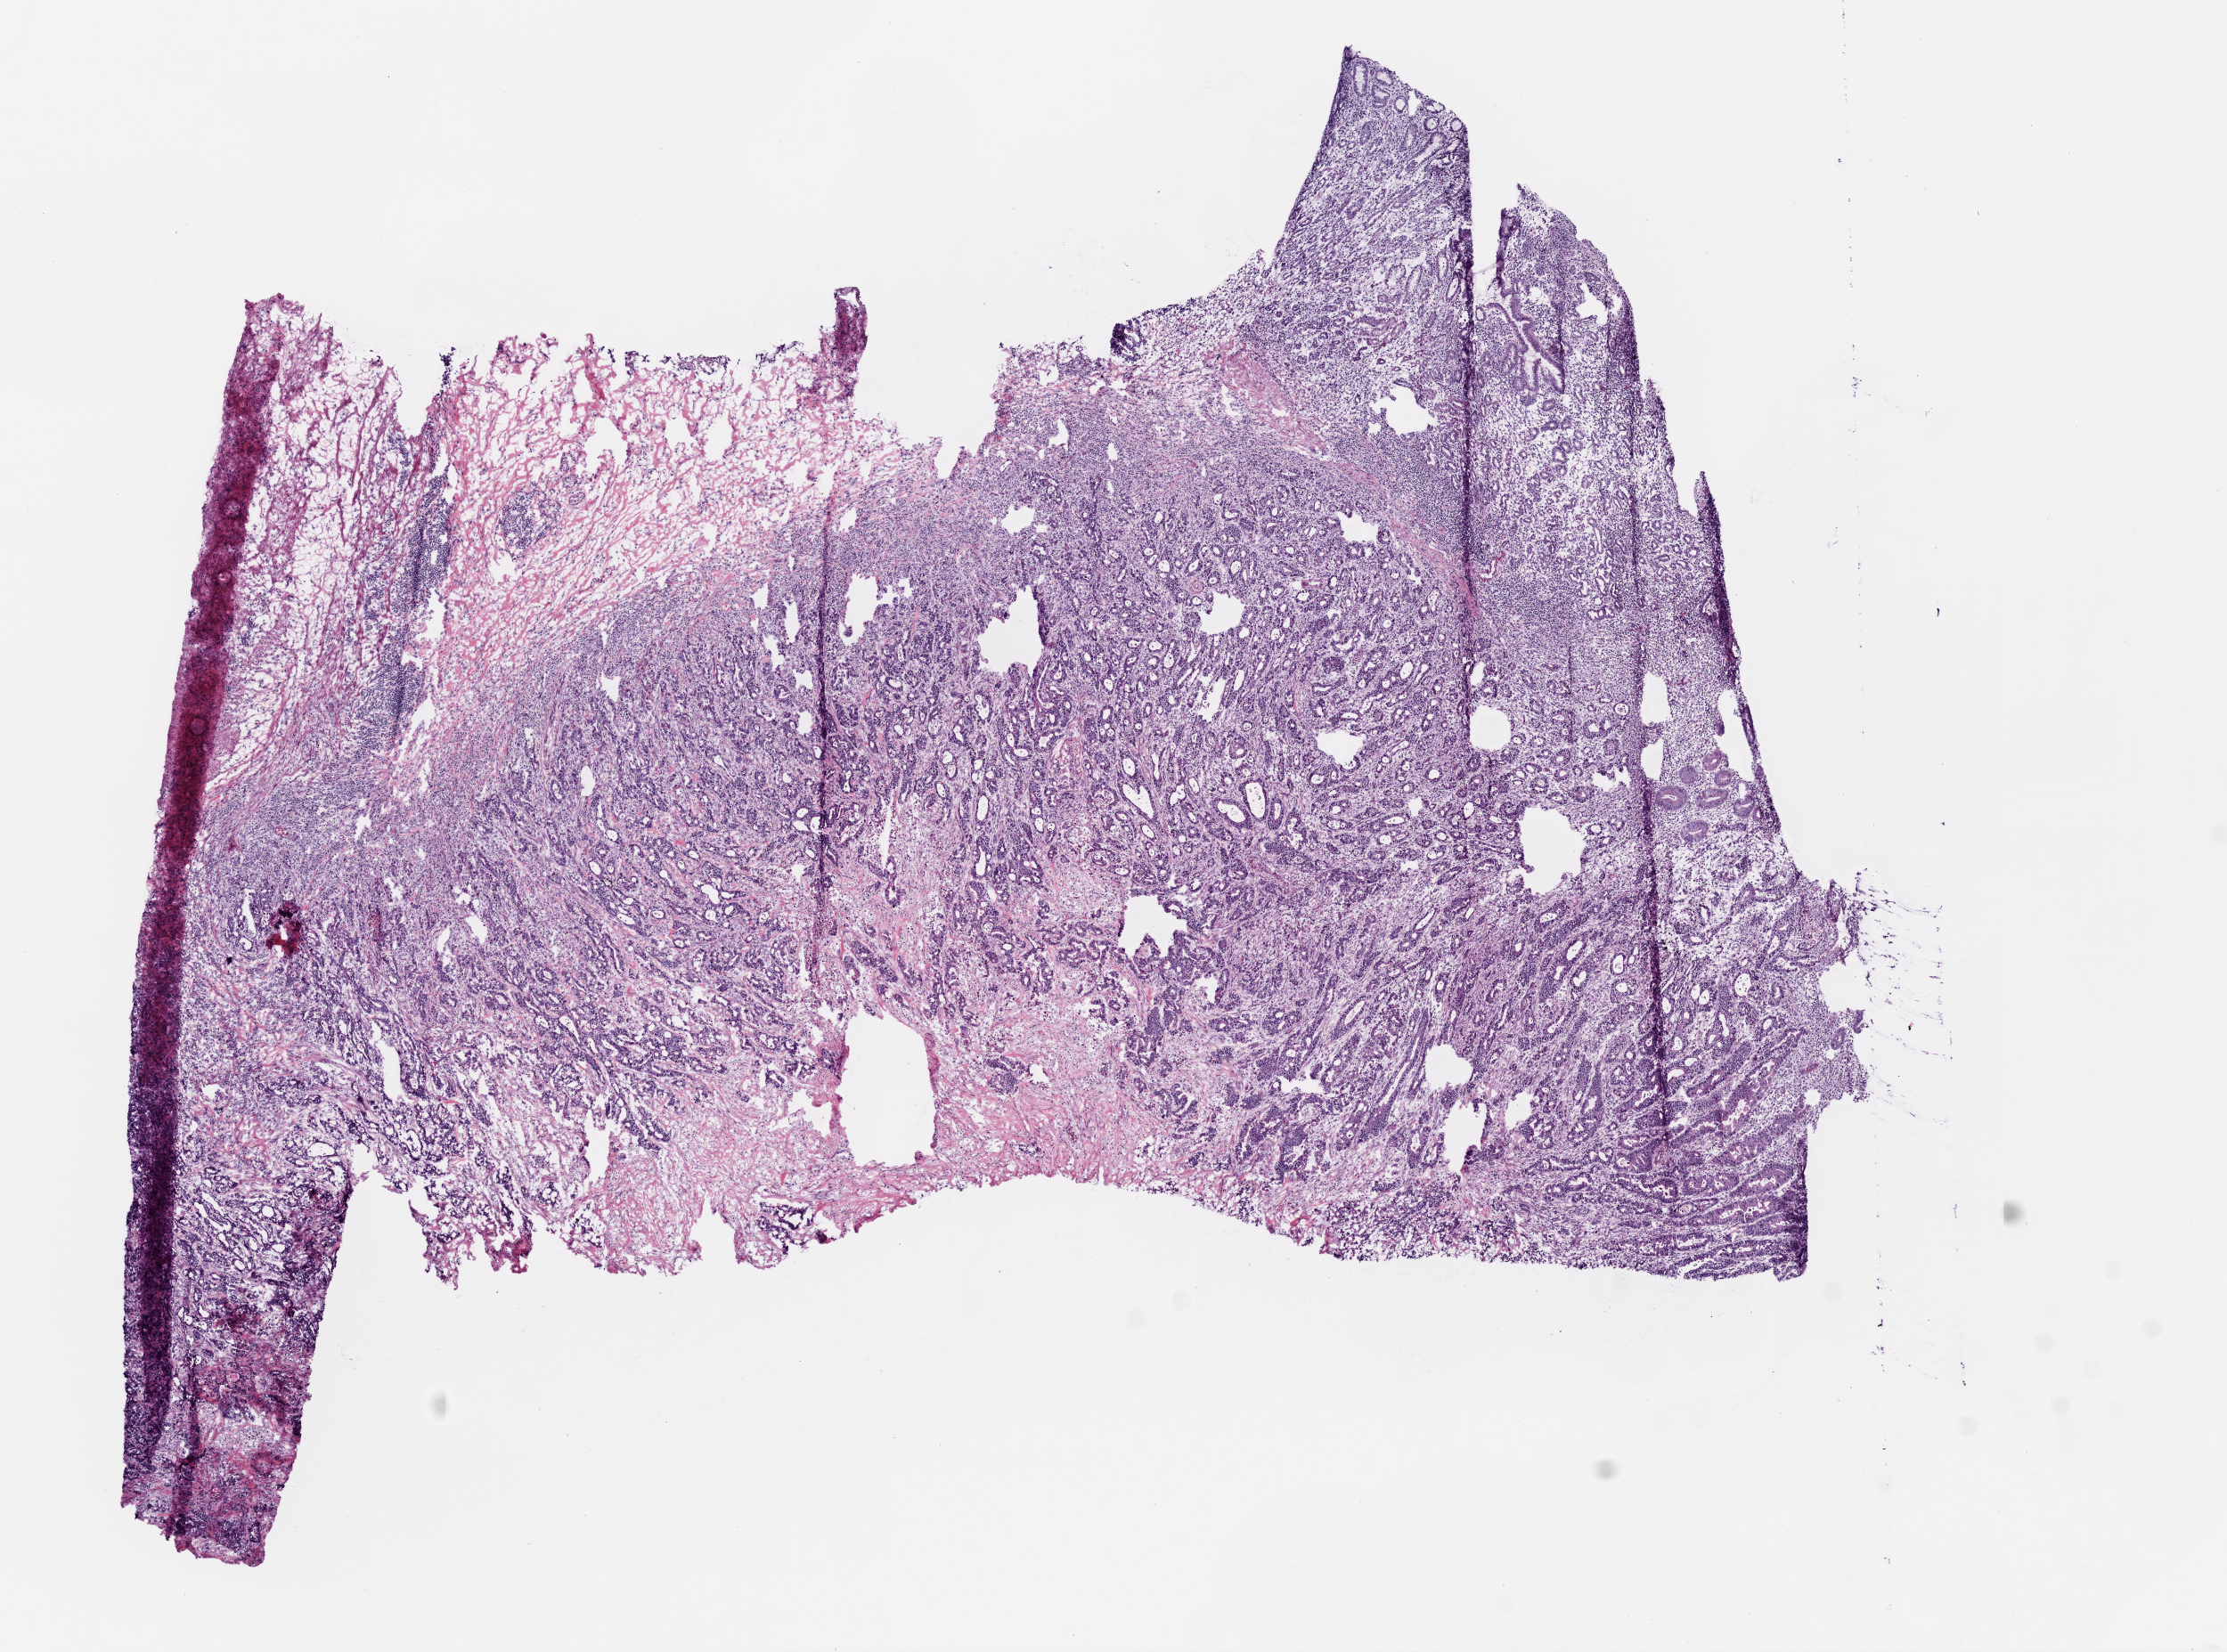
Whole-slide histology image, H&E, whole scanned area (about 10.0 x 7.4 mm, from a 20x scan) shown as a low-resolution overview; frozen section from the top of the tissue portion; stomach, primary tumour sample. Patient: male, age at initial diagnosis 83 years. Histologic grade: G2 (moderately differentiated). Pathologist review of this section (percent, as recorded): tumour cells 68%, tumour nuclei 60%, normal cells 20%, stromal cells 10%, necrosis 2%.
Lymph nodes positive (case pathology): 3 of 29 examined. AJCC pathologic stage: II. Diagnosis: Adenocarcinoma, intestinal type.